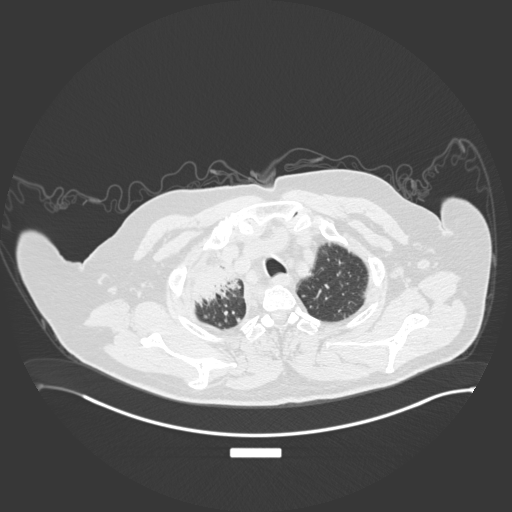
Chest CT, one axial slice; position 168 of 201 along the scan axis; reconstruction kernel B30f; 120 kVp; lung window (W 1500 / L -600 HU); 1 mm slice thickness; 512 × 512 image matrix. Male patient, age 69 years. From the clinical record (not read from this slice): clinical TNM (as recorded): T4 N3 M1.
Structures marked on this image (rectangle marked by the reading radiologist):
- lung tumour (recorded histology: adenocarcinoma): bounding box (x1, y1, x2, y2) in pixels: (186, 255, 238, 309)